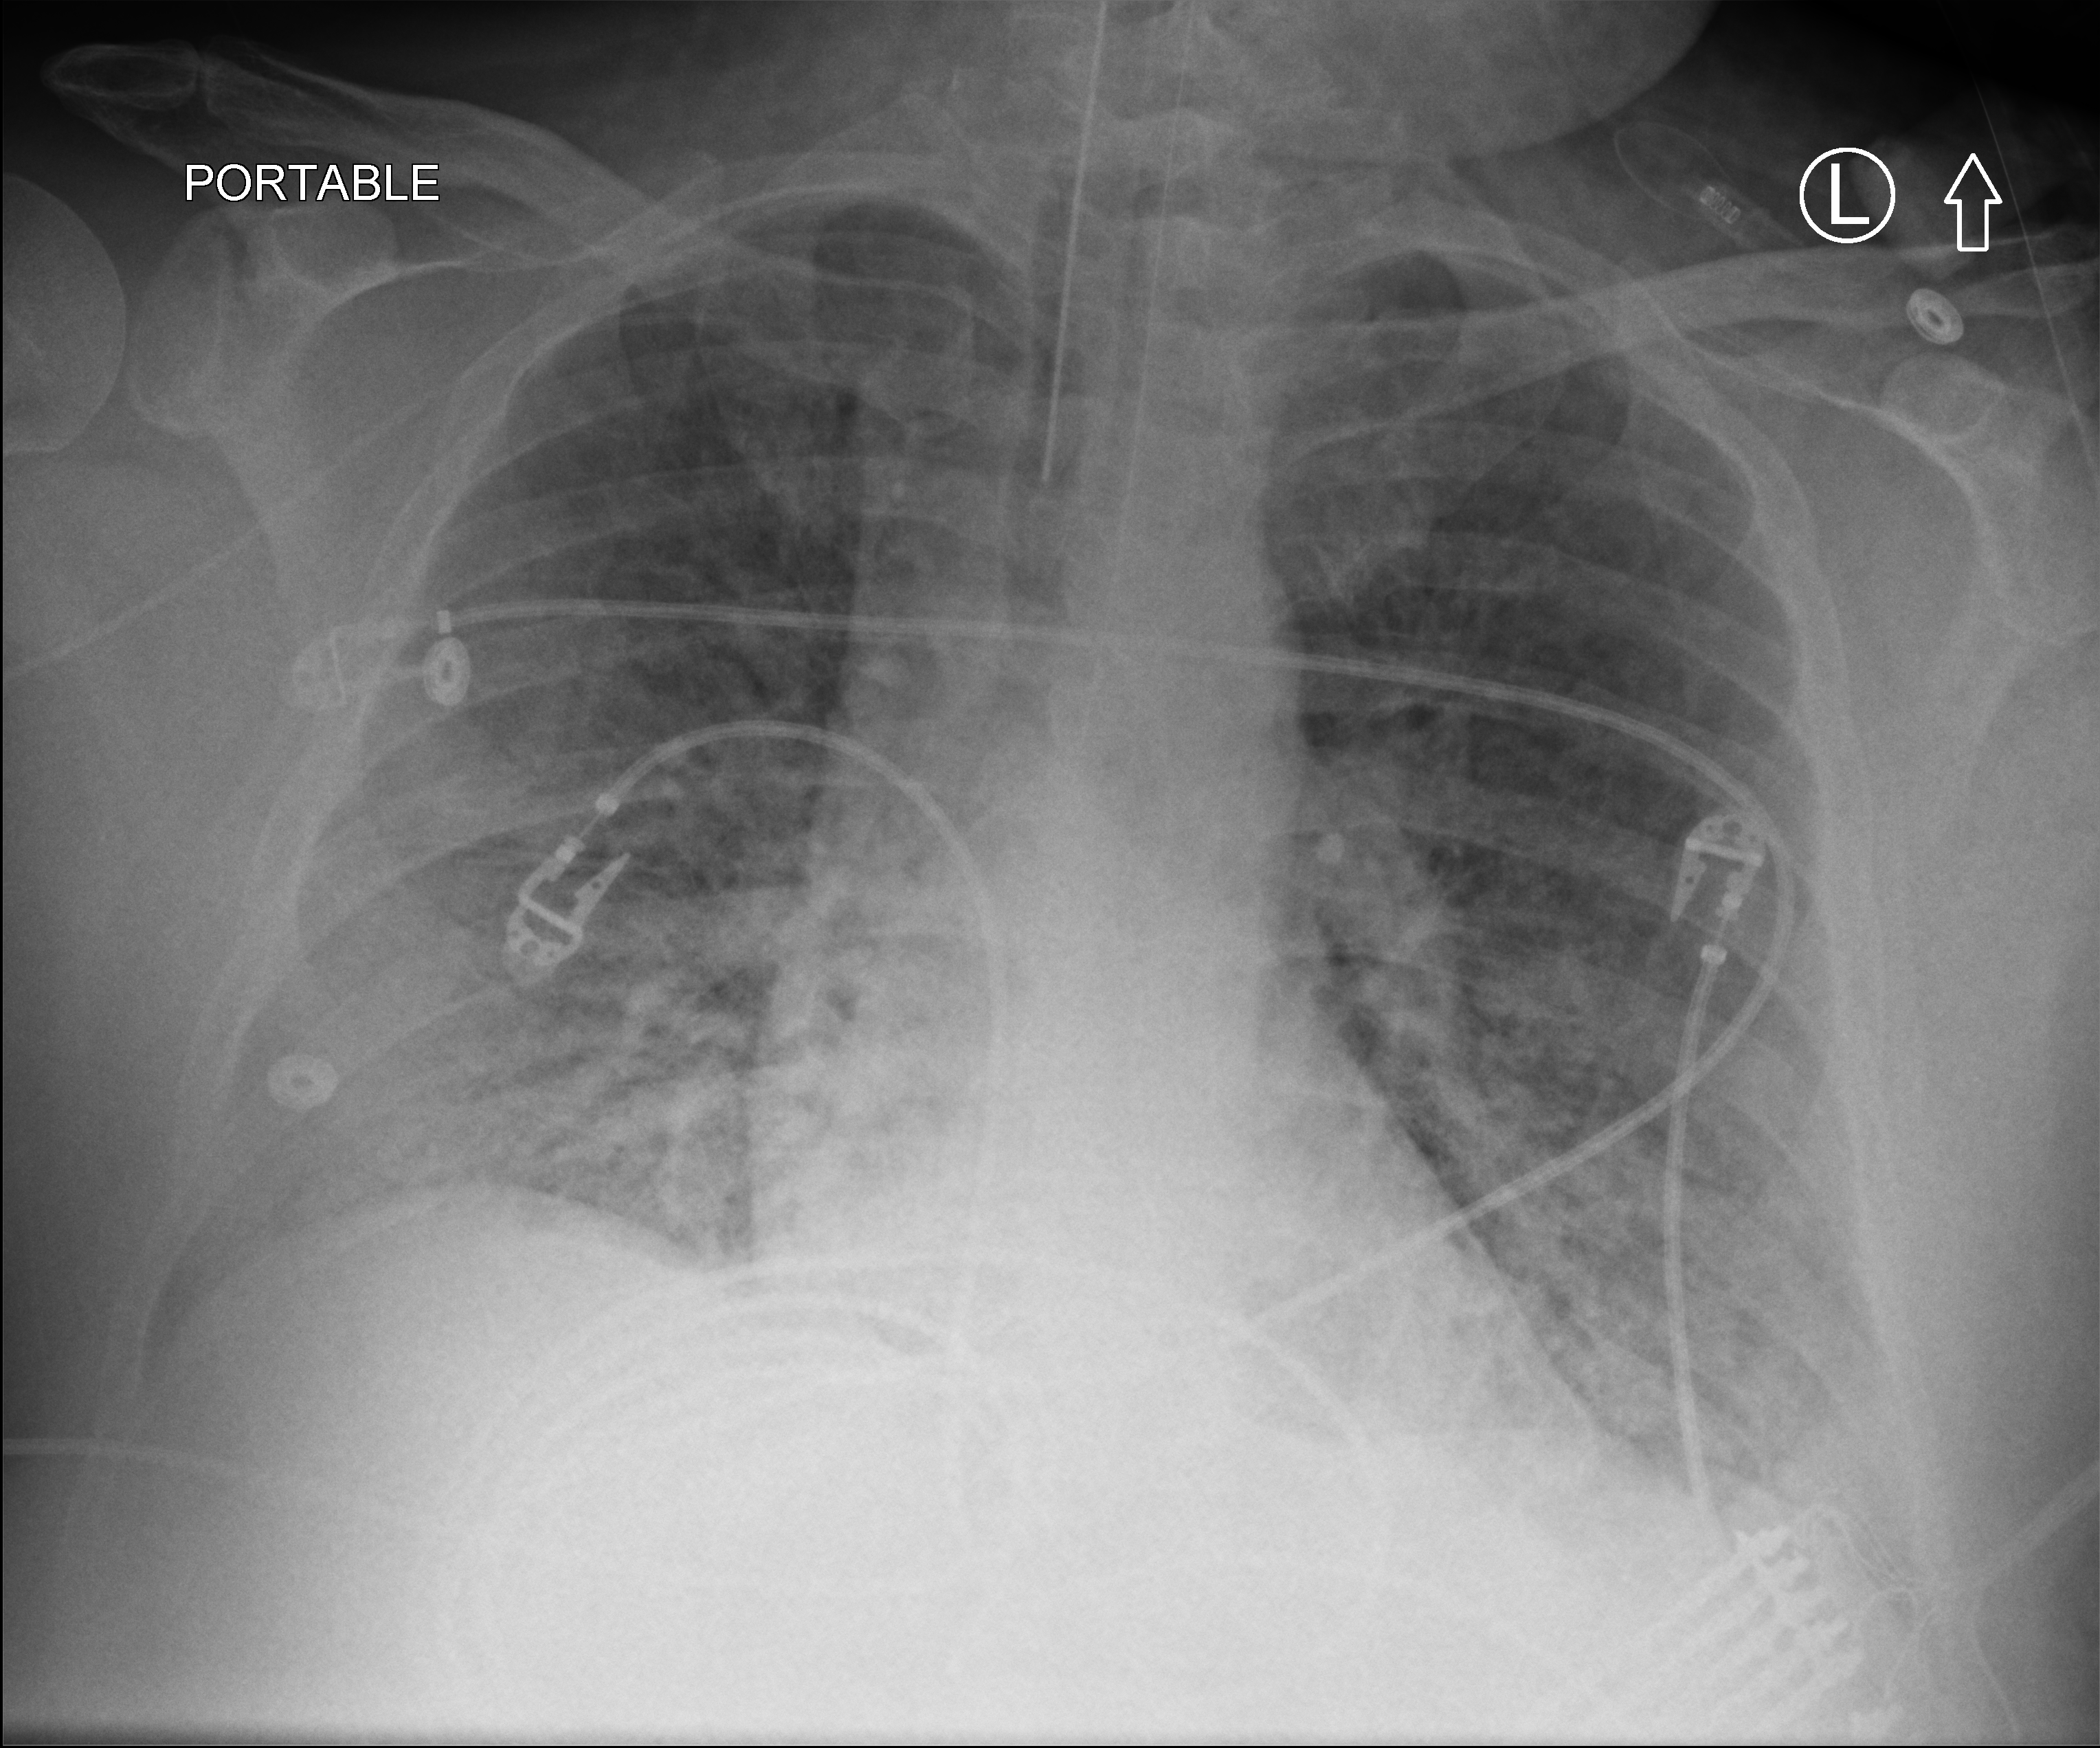
Portable chest radiograph; anteroposterior (AP) projection. Patient hospitalised with COVID-19, aged 18–59 years.
Admission-level facts for this patient (not findings on this image; timing relative to this image not recorded): diabetes (admission record): yes; admitted to intensive care during this hospital stay: yes.